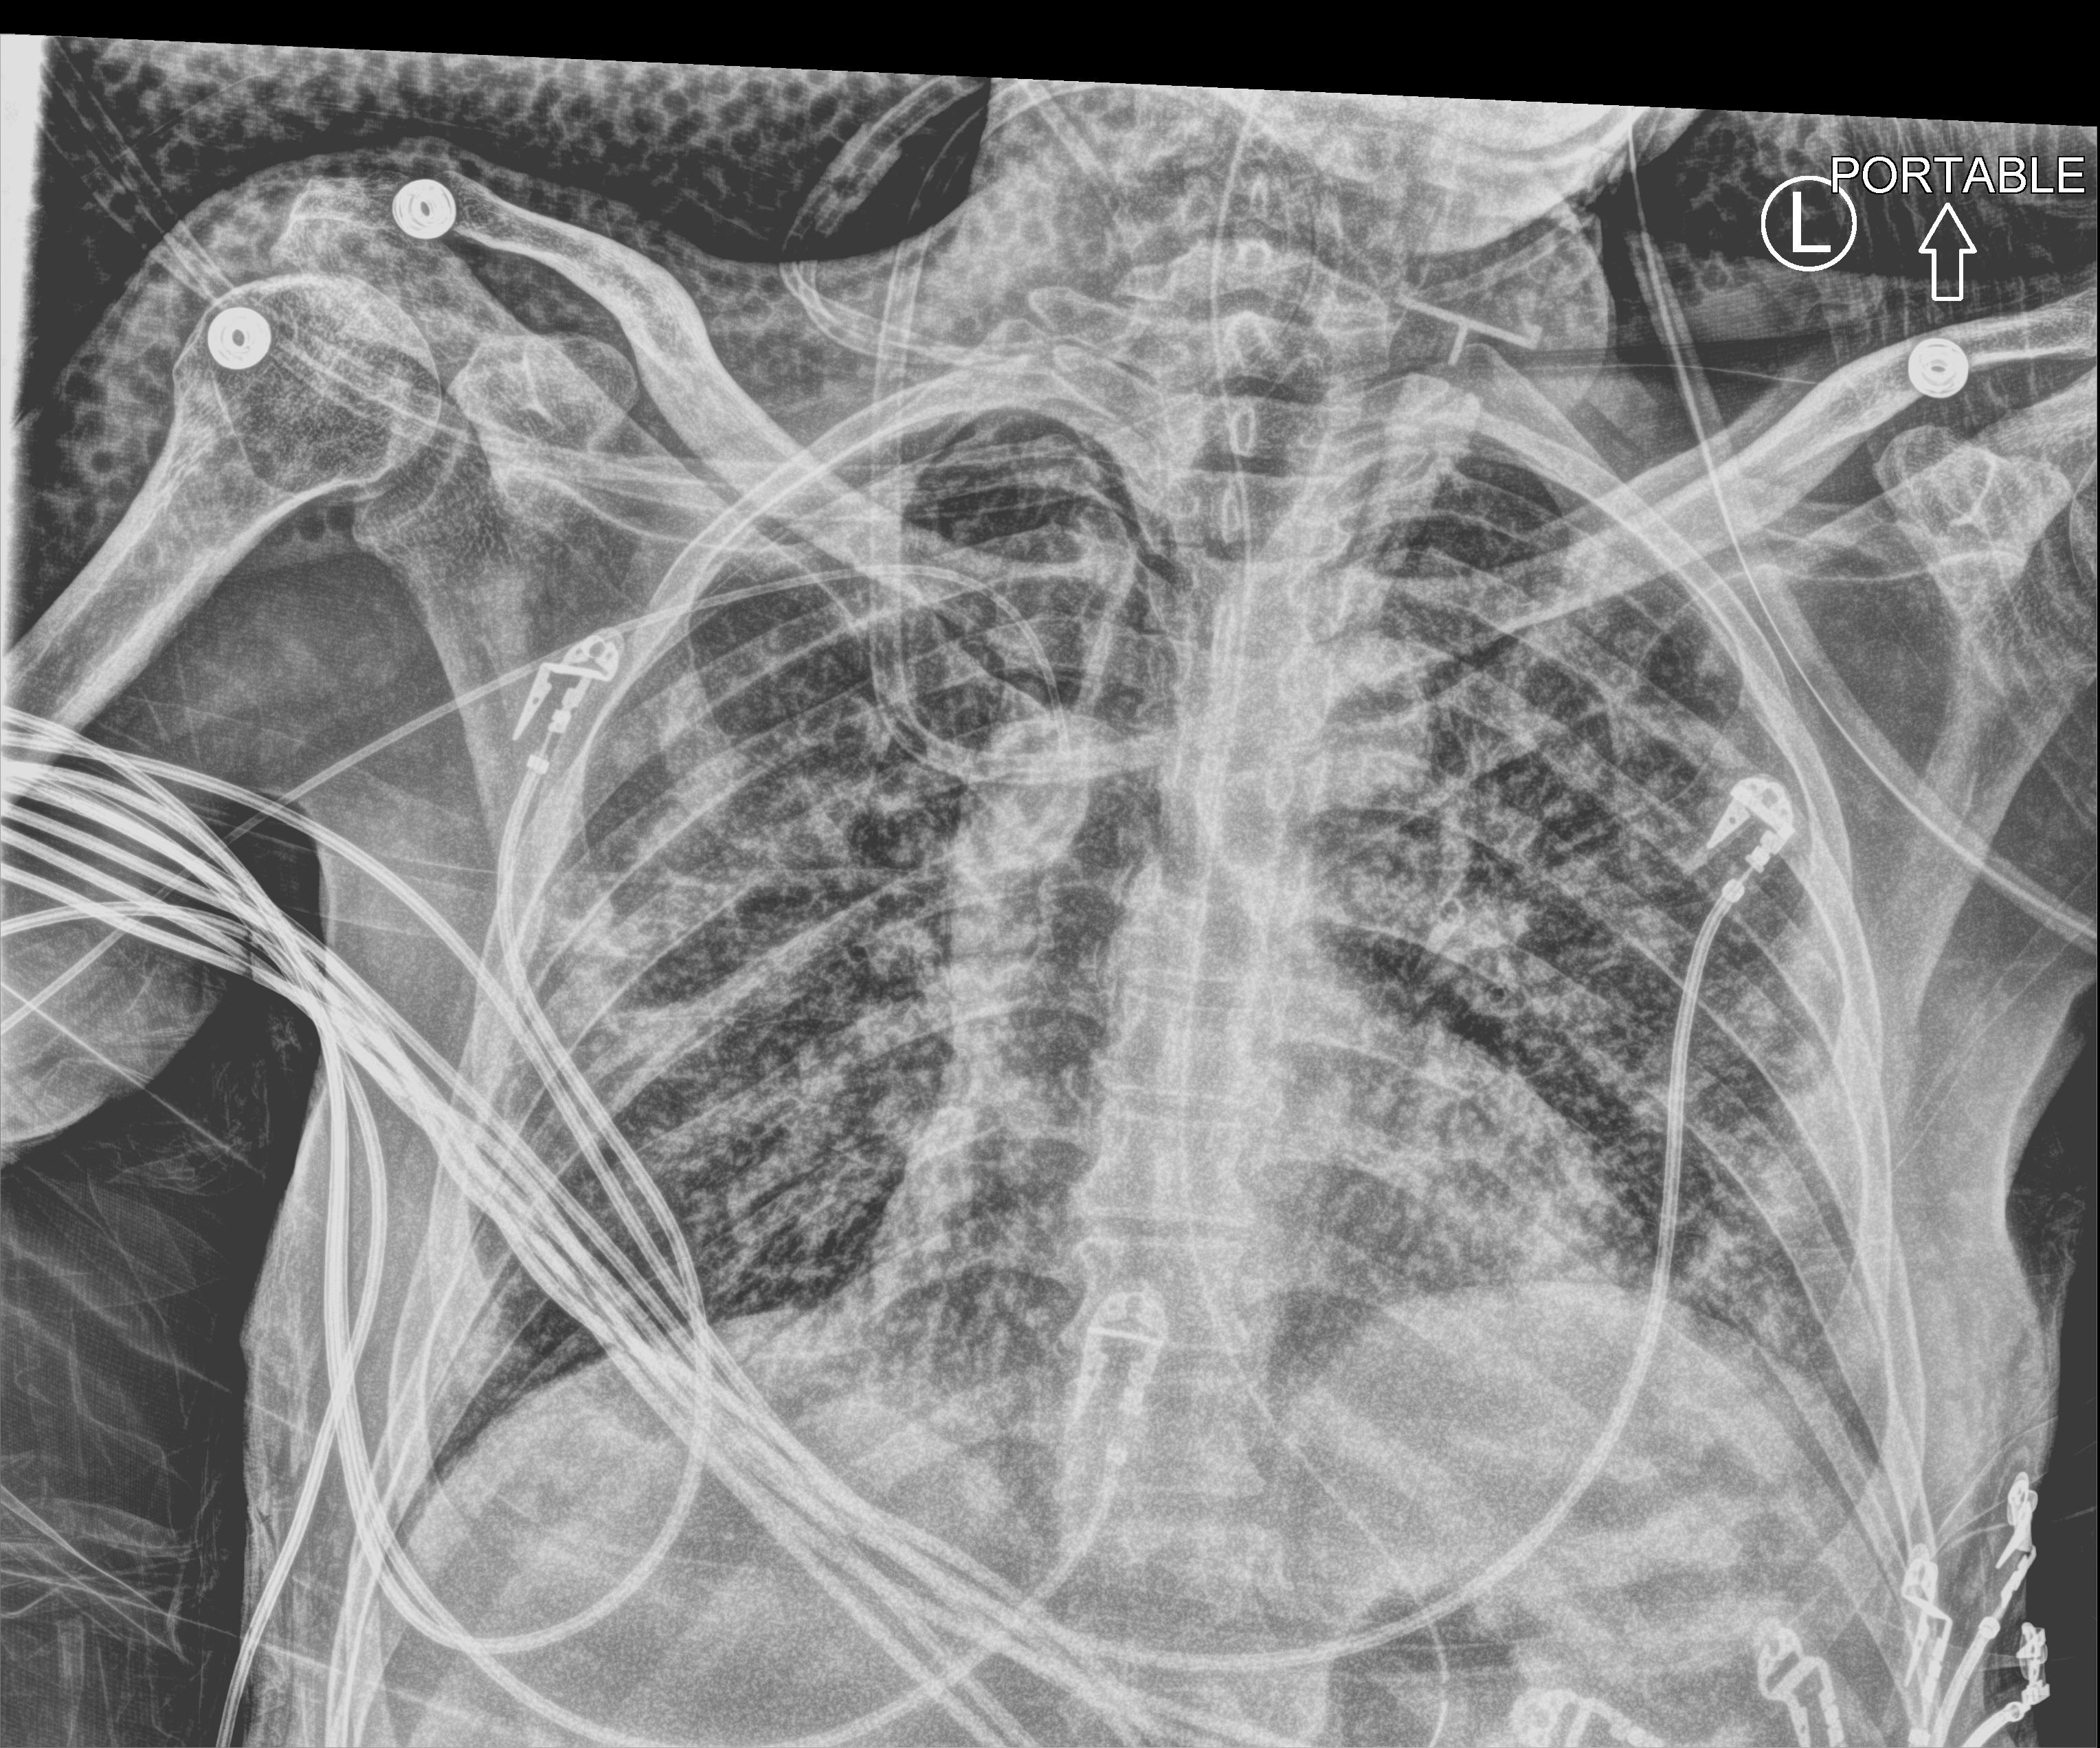
Chest X-ray (portable), anteroposterior (AP) projection. Patient hospitalised with COVID-19; male, aged 18–59 years.
From the hospital-stay record, not from the radiograph (when in the stay this image was taken is not recorded): length of hospital stay: 41 days; admitted to intensive care during this hospital stay: yes.